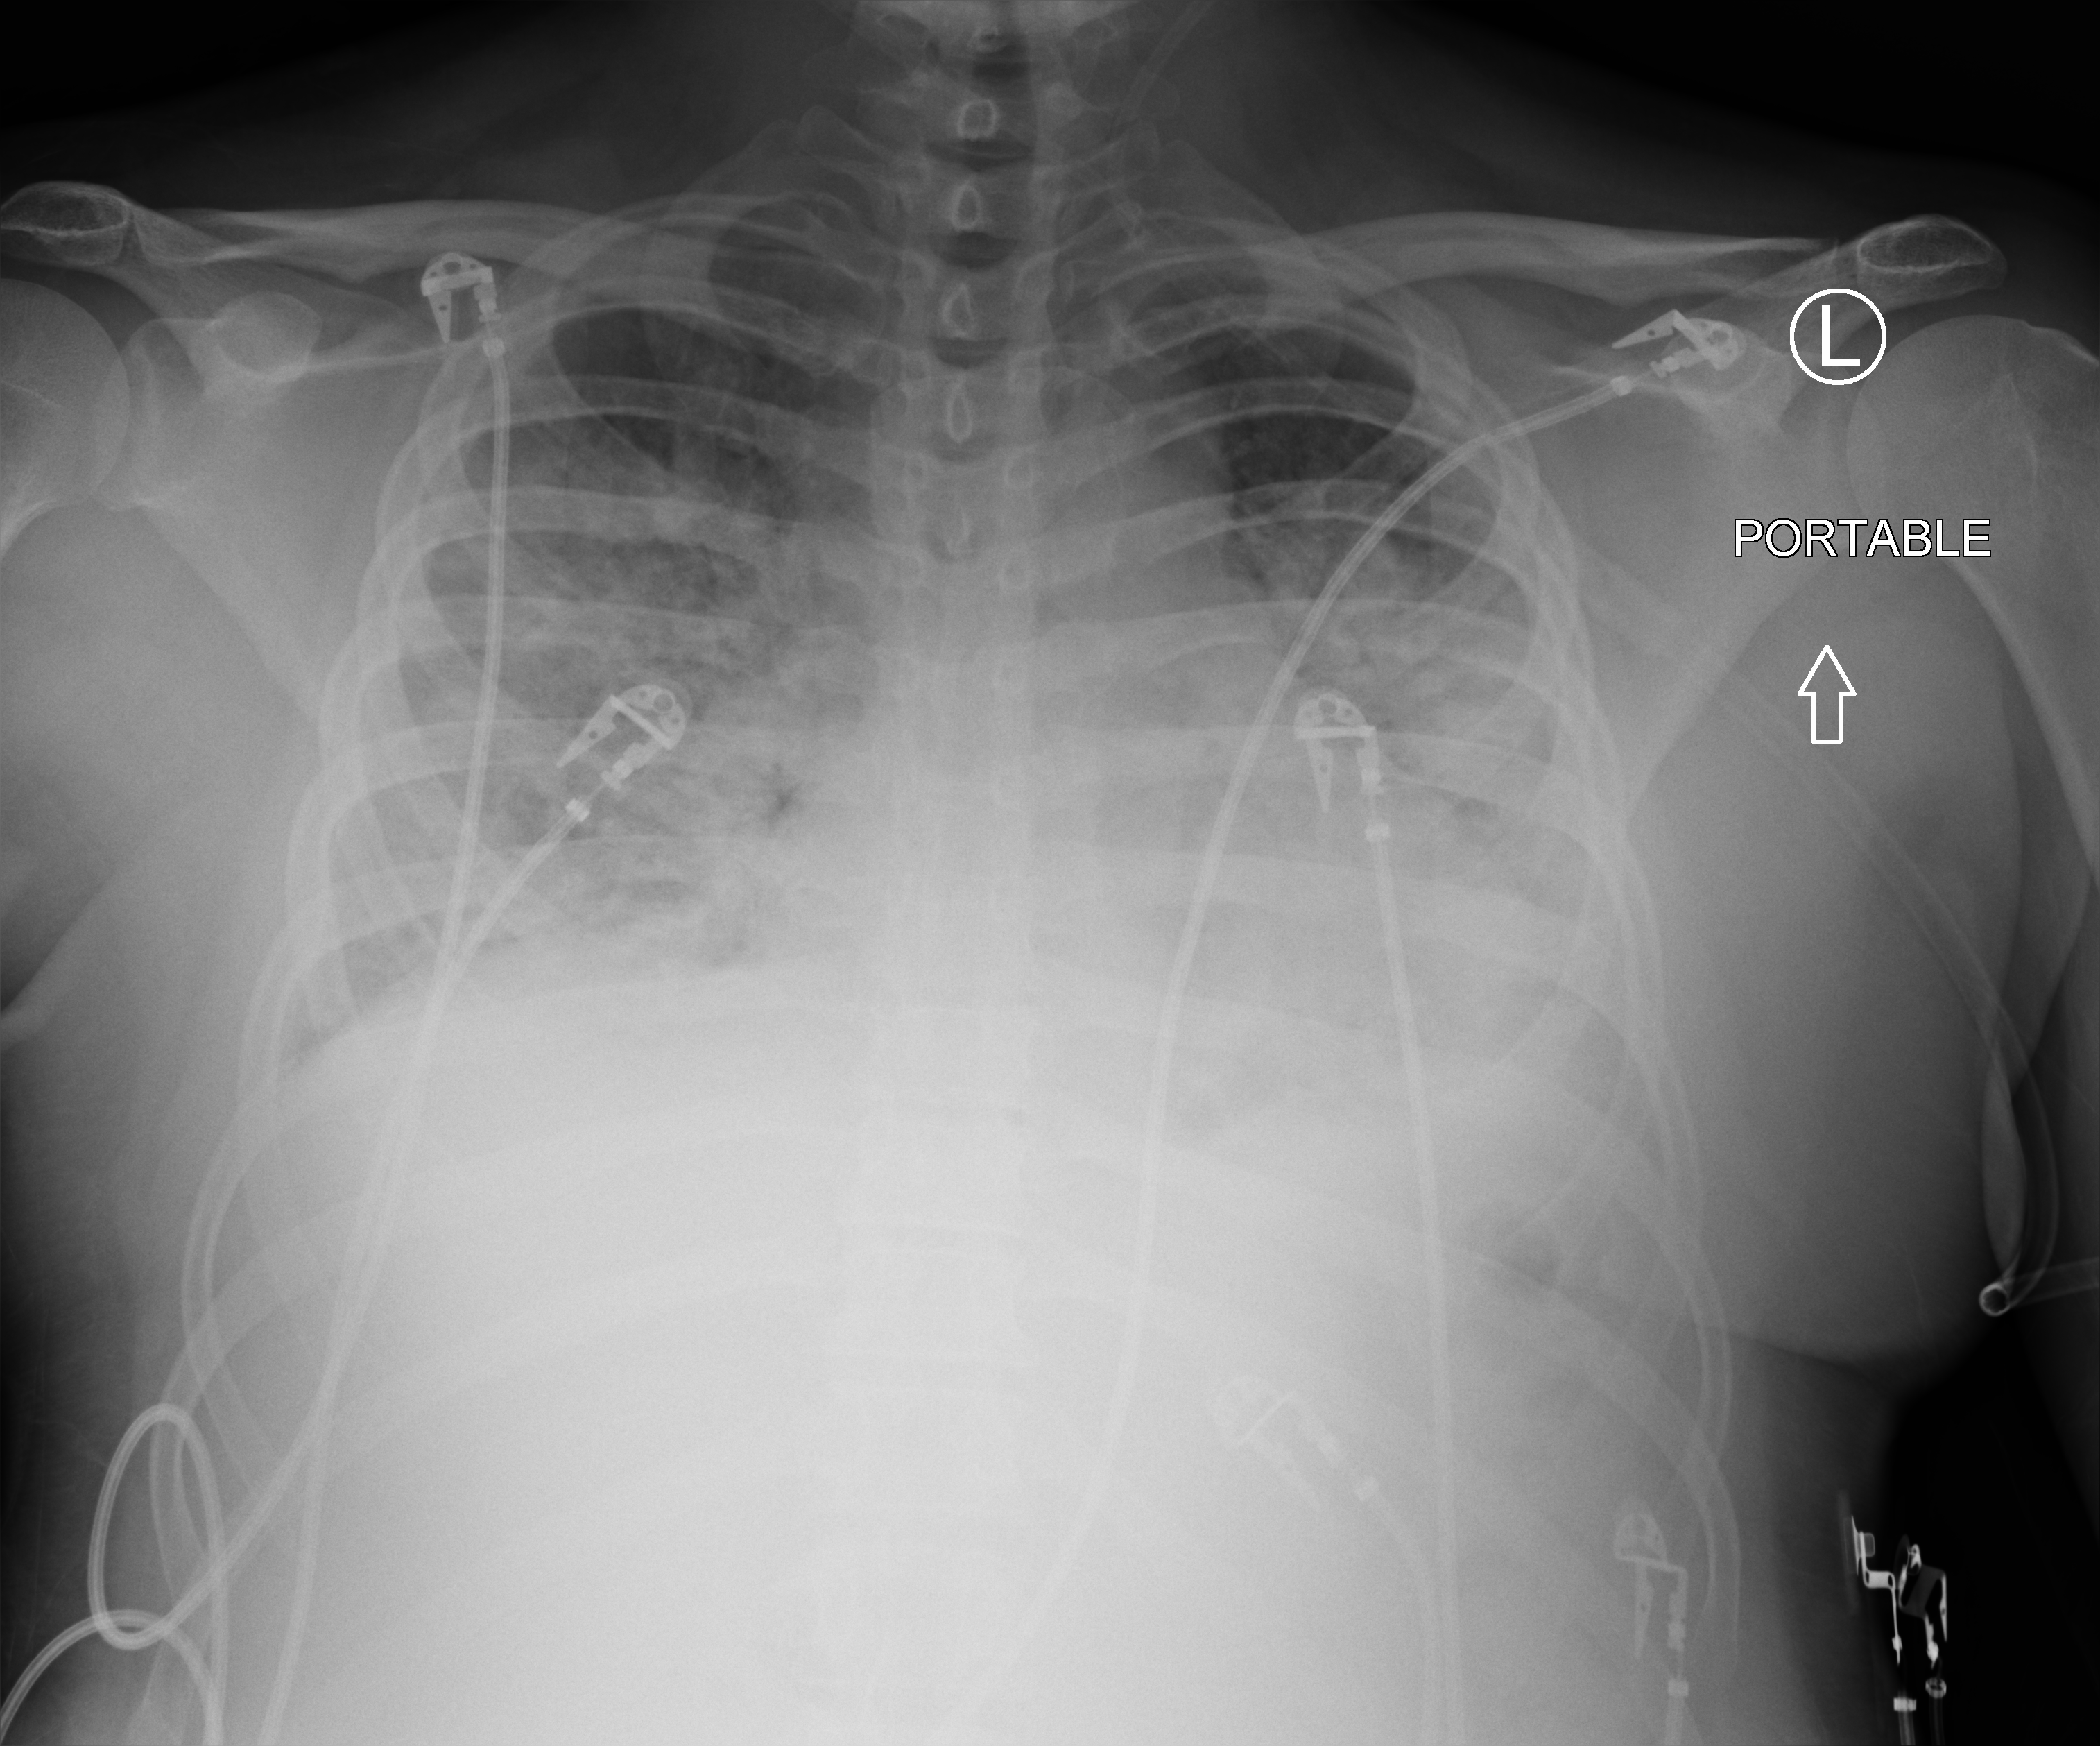
Portable chest radiograph. Patient hospitalised with COVID-19; male, aged 18–59 years.
Admission-level facts for this patient (not findings on this image; timing relative to this image not recorded): diabetes (admission record): yes; mechanically ventilated during this hospital stay: no; admitted to intensive care during this hospital stay: no.